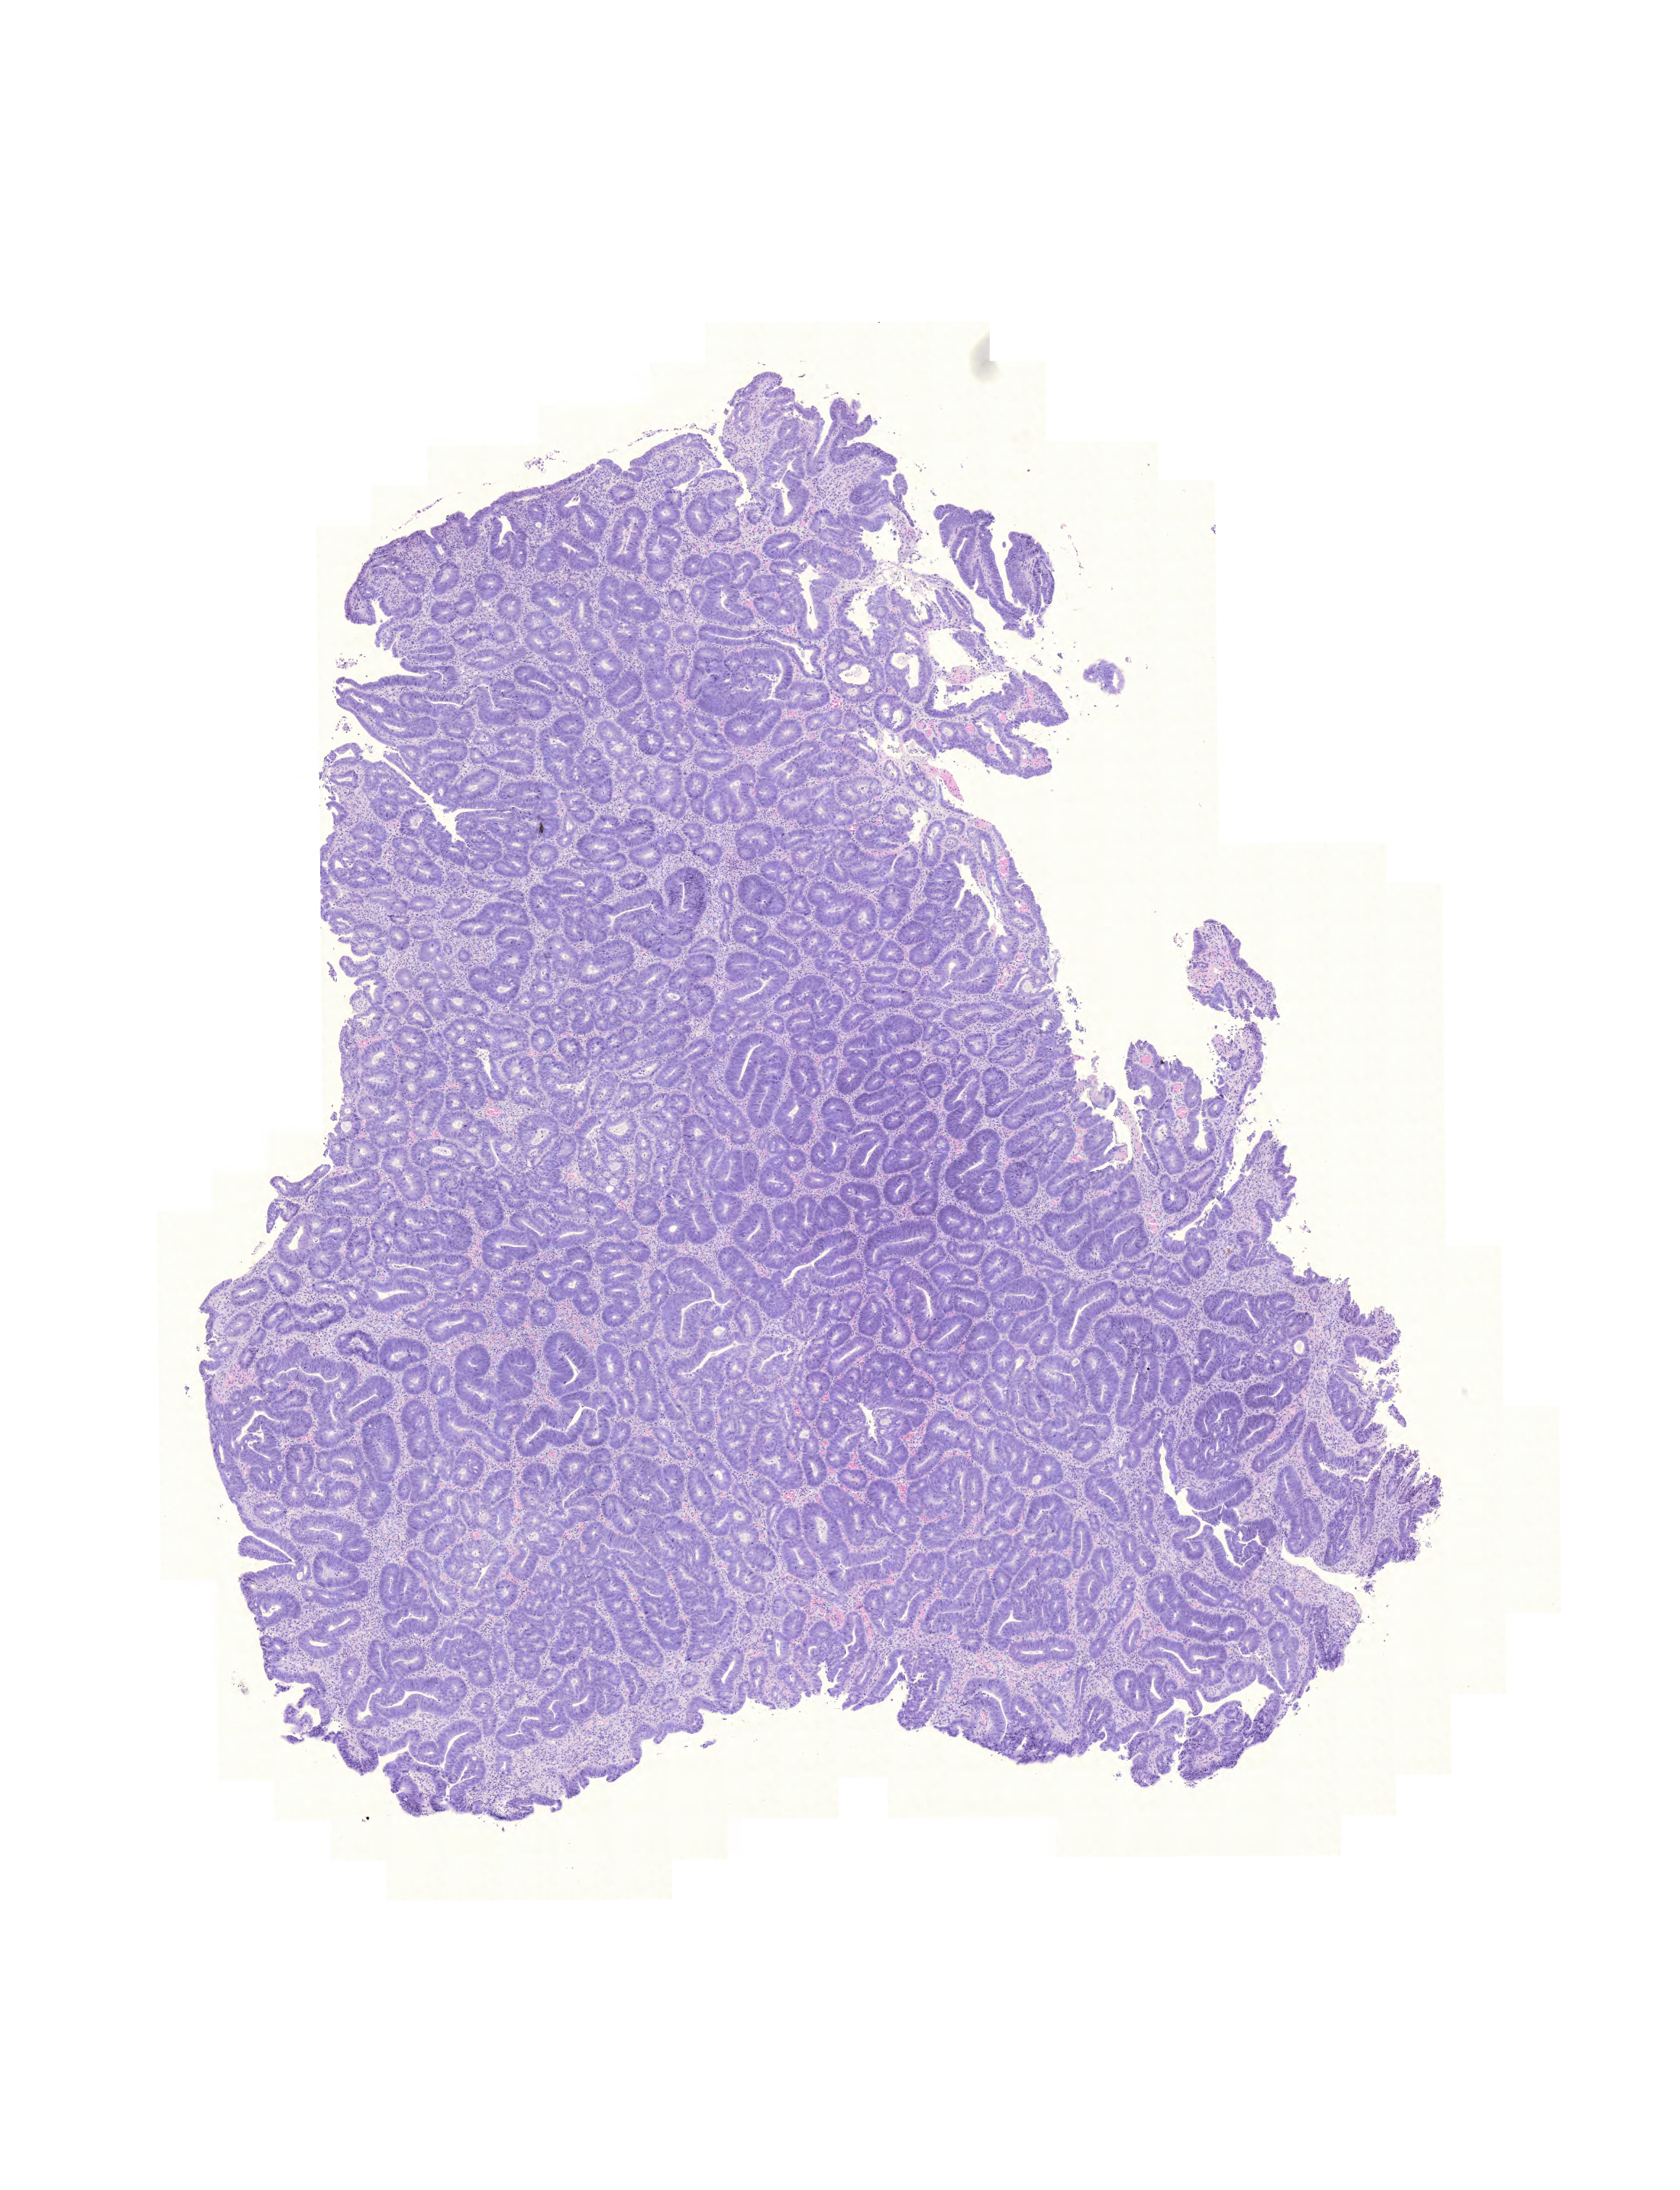
Whole-slide histology image, H&E — shown as a low-resolution overview of the whole scanned area (about 8.6 x 11.2 mm, slide scanned at 20x). Formalin-fixed paraffin-embedded (FFPE) diagnostic section. Rectum, primary tumour sample. Male, age 65 years at initial diagnosis.
- histologic diagnosis: Adenocarcinoma, NOS
- TNM: T3 N0 M0
- AJCC pathologic stage: IIA
- lymph nodes positive (case pathology): 0 of 15 examined